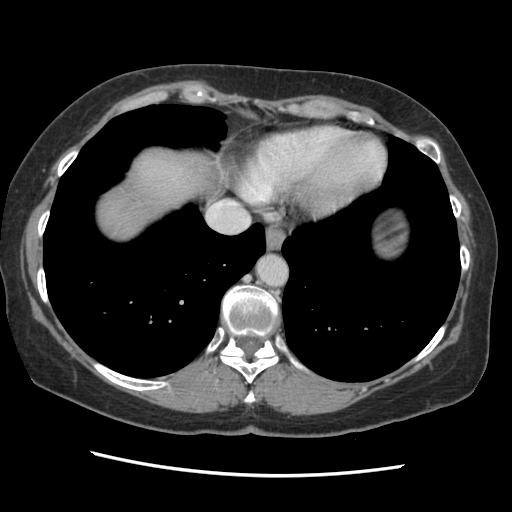
Contrast-enhanced abdominal CT, one axial slice. Slice 125 of 141 in the series (ordered by position). 120 kVp. Soft-tissue window (W 400 / L 40 HU). 512 × 512 image matrix. Female patient, age 61 years. Case-level facts recorded for this patient, not image findings: diagnosis: colorectal cancer liver metastases, imaged before liver resection; multiple liver metastases: no; largest metastasis: 2.4 cm; disease in both lobes: no.
Structures marked on this image (outlined manually by an expert reader):
- liver: box from (x=95, y=147) to (x=218, y=240) px
- planned liver remnant (the part of the liver to remain after resection): (x=95, y=147)–(x=218, y=240)